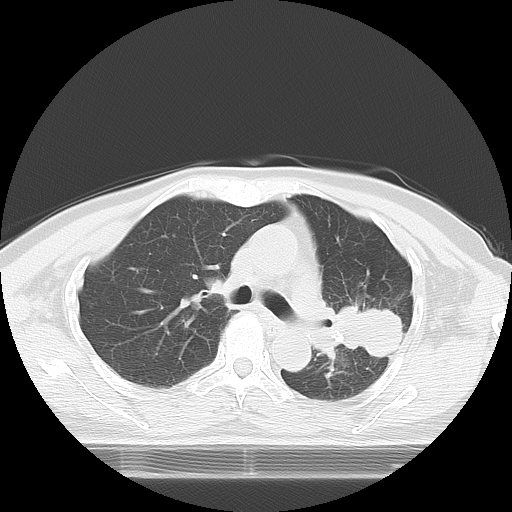
Chest CT, one axial slice; slice 3 of 21 in the series (ordered by position); reconstruction kernel LUNG; 120 kVp; lung window (W 1500 / L -600 HU); 5 mm slice thickness; 512 × 512 image matrix. Female patient, age 74 years. Case-level facts recorded for this patient, not image findings: clinical TNM (as recorded): T3 N1 M1c; histopathological grade: G3.
Outlined on this slice (bounding box drawn by a radiologist):
- lung tumour (recorded histology: small cell carcinoma): bounding box [x1, y1, x2, y2] px = [322, 291, 420, 366]